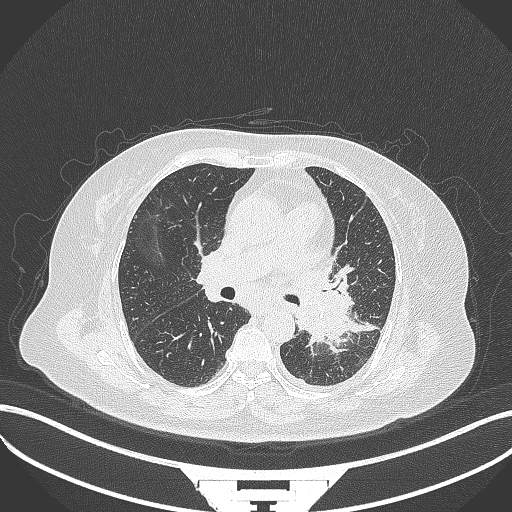
Chest CT, one axial slice; position 195 of 322 along the scan axis; reconstruction kernel B70f; 120 kVp; lung window (W 1500 / L -600 HU); 1 mm slice thickness; 512 × 512 image matrix. Patient: female, 69 years. From the clinical record (not read from this slice): clinical TNM (as recorded): T2b N3 M1.
Outlined on this slice (rectangle marked by the reading radiologist):
- lung tumour (recorded histology: adenocarcinoma): box from (x=291, y=283) to (x=352, y=346) px